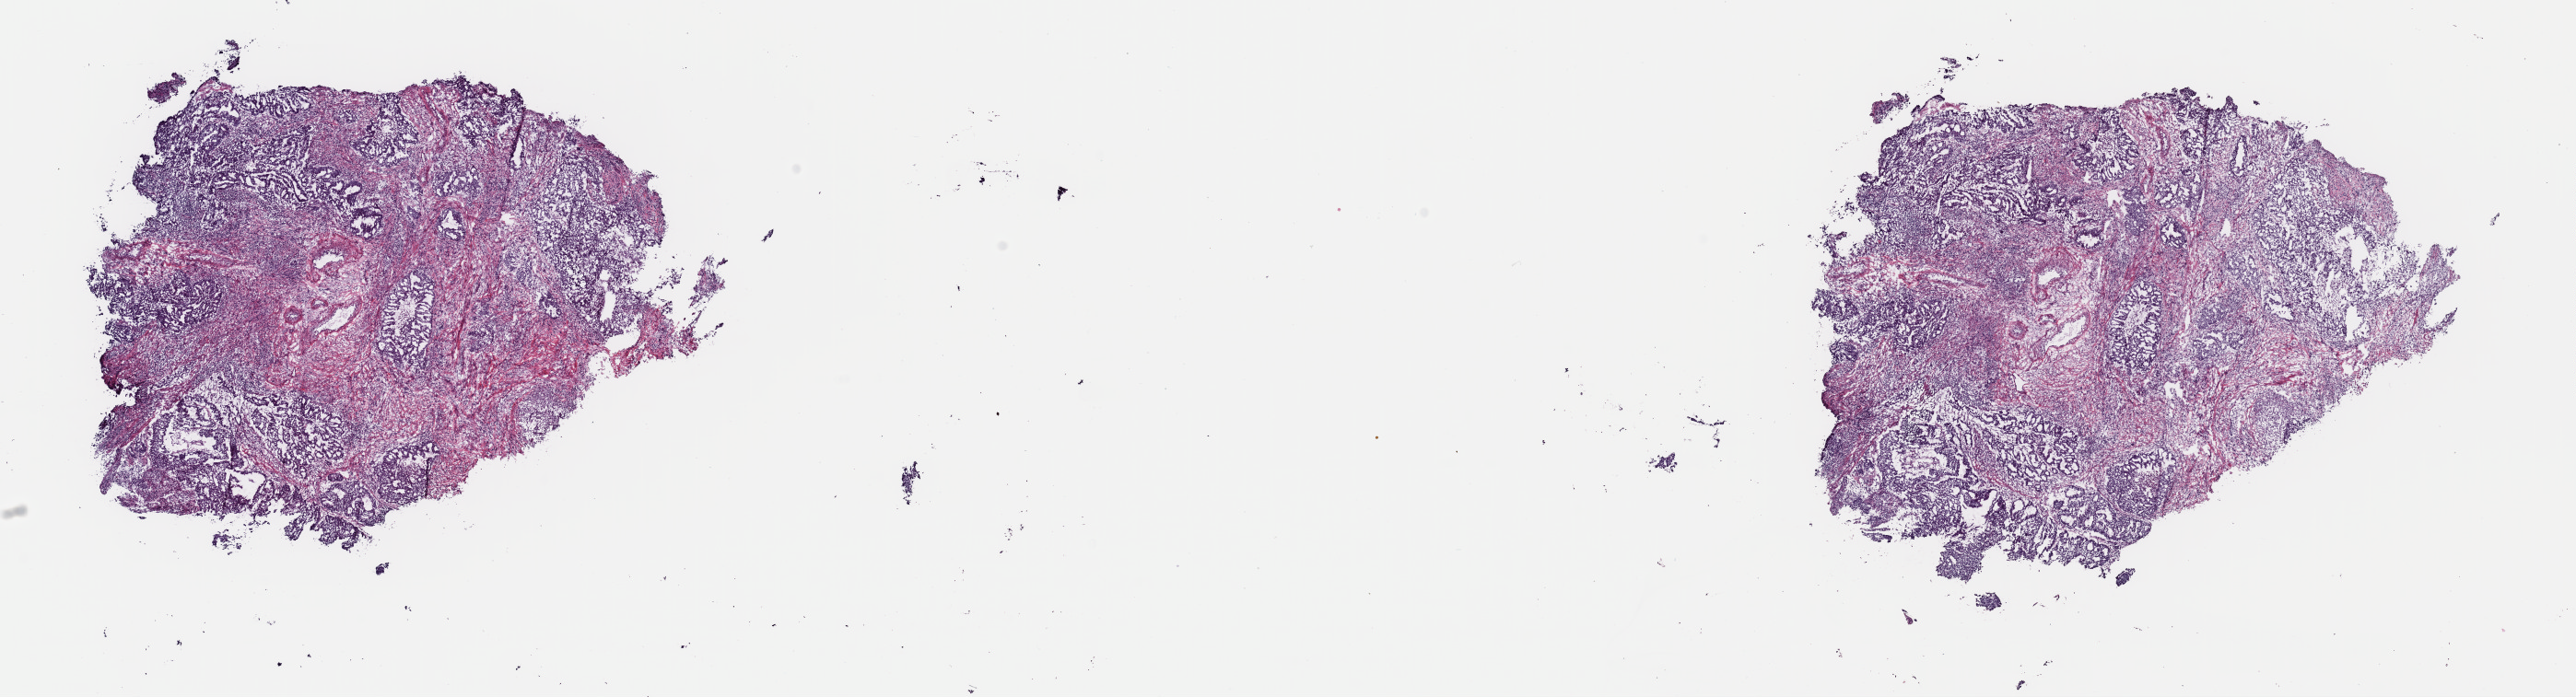
H&E whole-slide image — whole scanned area (about 22.1 x 6.0 mm) shown as a low-resolution overview, frozen section, sample: primary tumour, uterus. Female patient; age at initial diagnosis 53 years. Histologic grade: G3 (poorly differentiated). Pathologist review of this section (percent, as recorded): tumour cells 90%, tumour nuclei 85%, normal cells 5%, stromal cells 0%, necrosis 5%. Infiltration values recorded for this section: lymphocyte infiltration 4%, monocyte infiltration 0%, neutrophil infiltration 0%.
FIGO stage: IA. Pathologic diagnosis: Serous cystadenocarcinoma, NOS (endometrium).